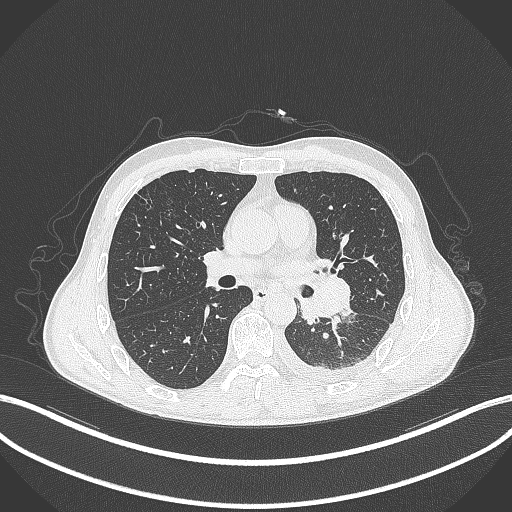
Chest CT, one axial slice; slice 176 of 295 in the series (ordered by position); reconstruction kernel B70f; lung window (W 1500 / L -600 HU); 512 × 512 image matrix, field of view 400 × 400 mm. Patient: male, 47 years. Case-level facts recorded for this patient, not image findings: clinical TNM (as recorded): T3 N1 M1c; histopathological grade: G3.
Outlined on this slice (bounding box drawn by a radiologist):
- lung tumour (recorded histology: small cell carcinoma): bounding box (x1, y1, x2, y2) in pixels: (291, 271, 352, 326)